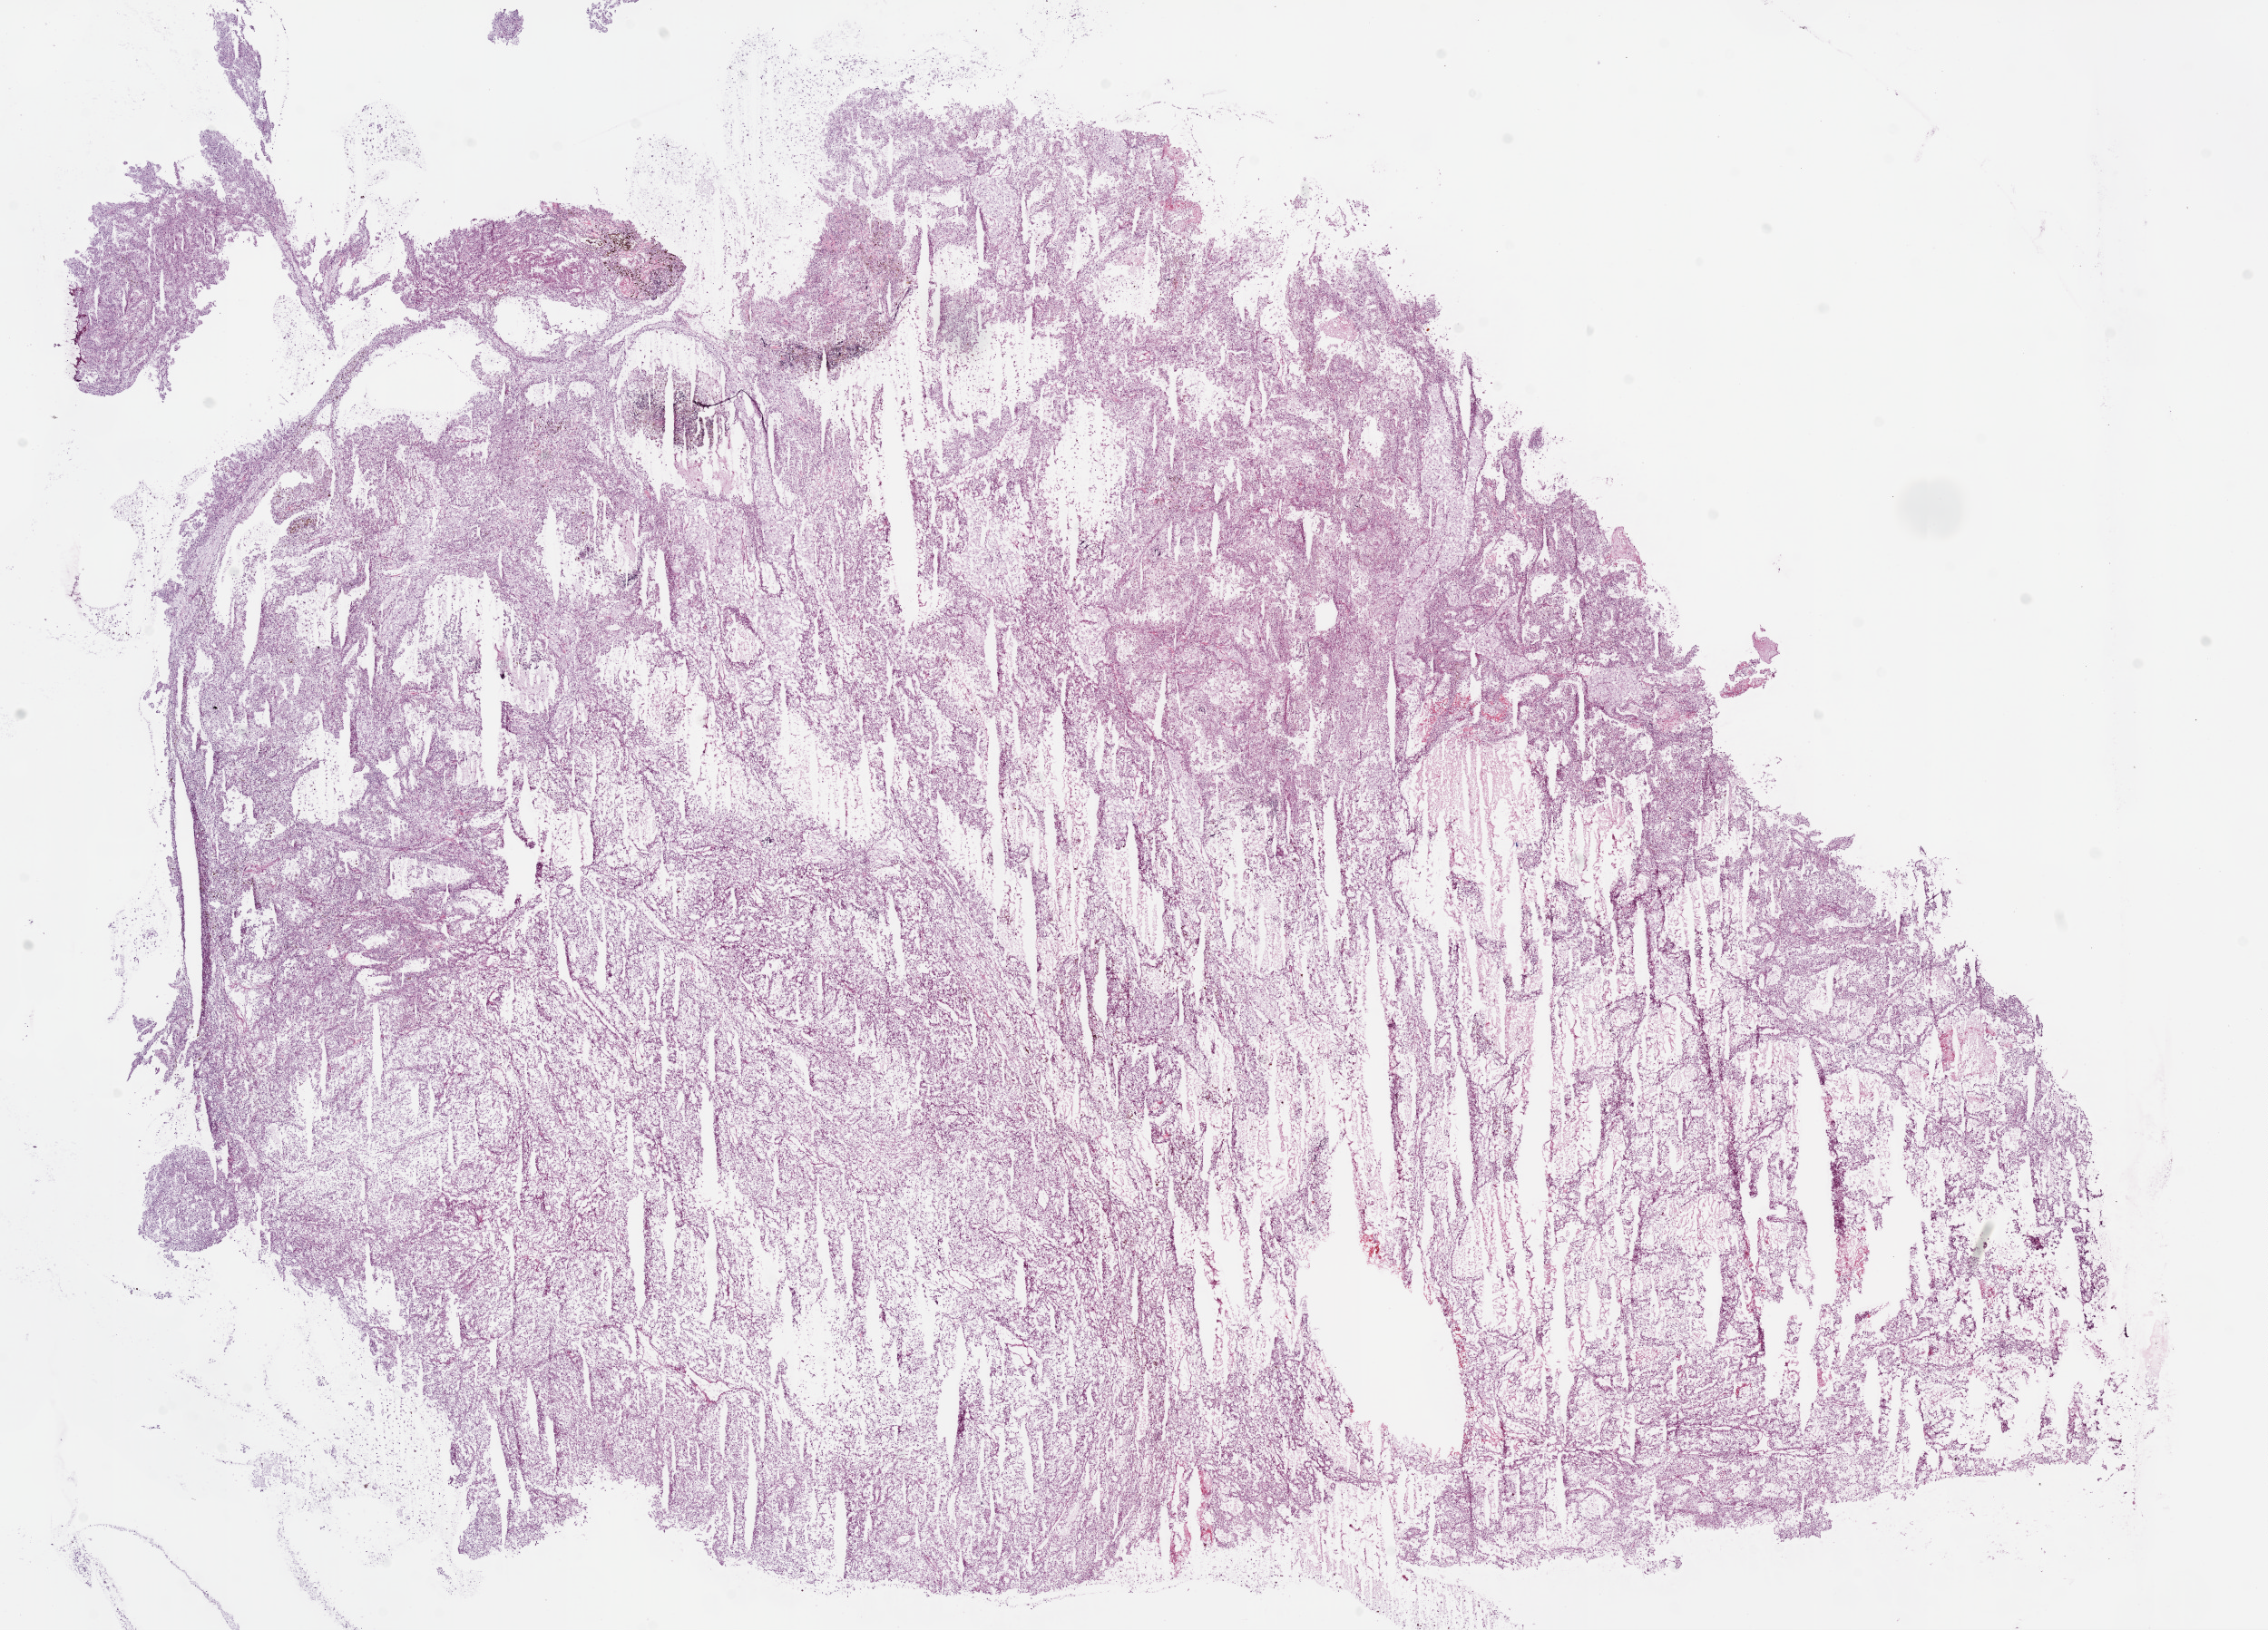
Digitized H&E tissue section (whole slide), shown as a low-resolution overview of the whole scanned area (about 20.1 x 14.4 mm, acquisition: 20x scan). Frozen section. Kidney, primary tumour sample. Female, age 77 years at initial diagnosis.
Diagnosis: Clear cell adenocarcinoma, NOS.